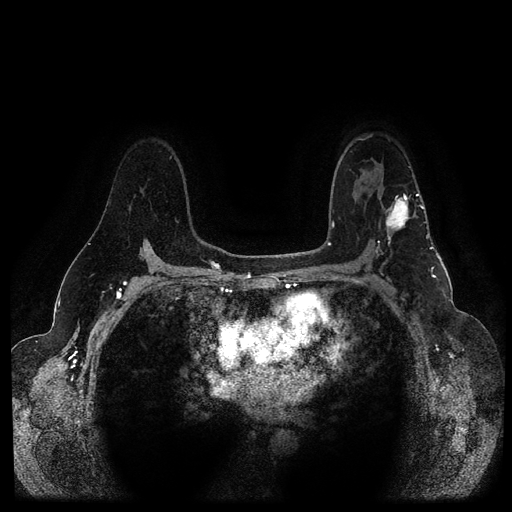
Breast MRI (dynamic contrast-enhanced, multi-phase), one axial slice; position 72 of 116 along the scan axis; dynamic contrast-enhanced series, time point 2 of 5 at this slice position (early post-contrast); 1.5 T; TE 2.6 ms, TR 5.3 ms; 512 × 512 image matrix. Female patient, age 54 years.
Annotated regions visible in this slice (semi-automatic segmentation, software-assisted and operator-edited):
- breast lesion (labelled 'tumour' in the annotation; benign lesions carry a separate 'benign' label): bounding box (x1, y1, x2, y2) in pixels: (383, 193, 411, 234)